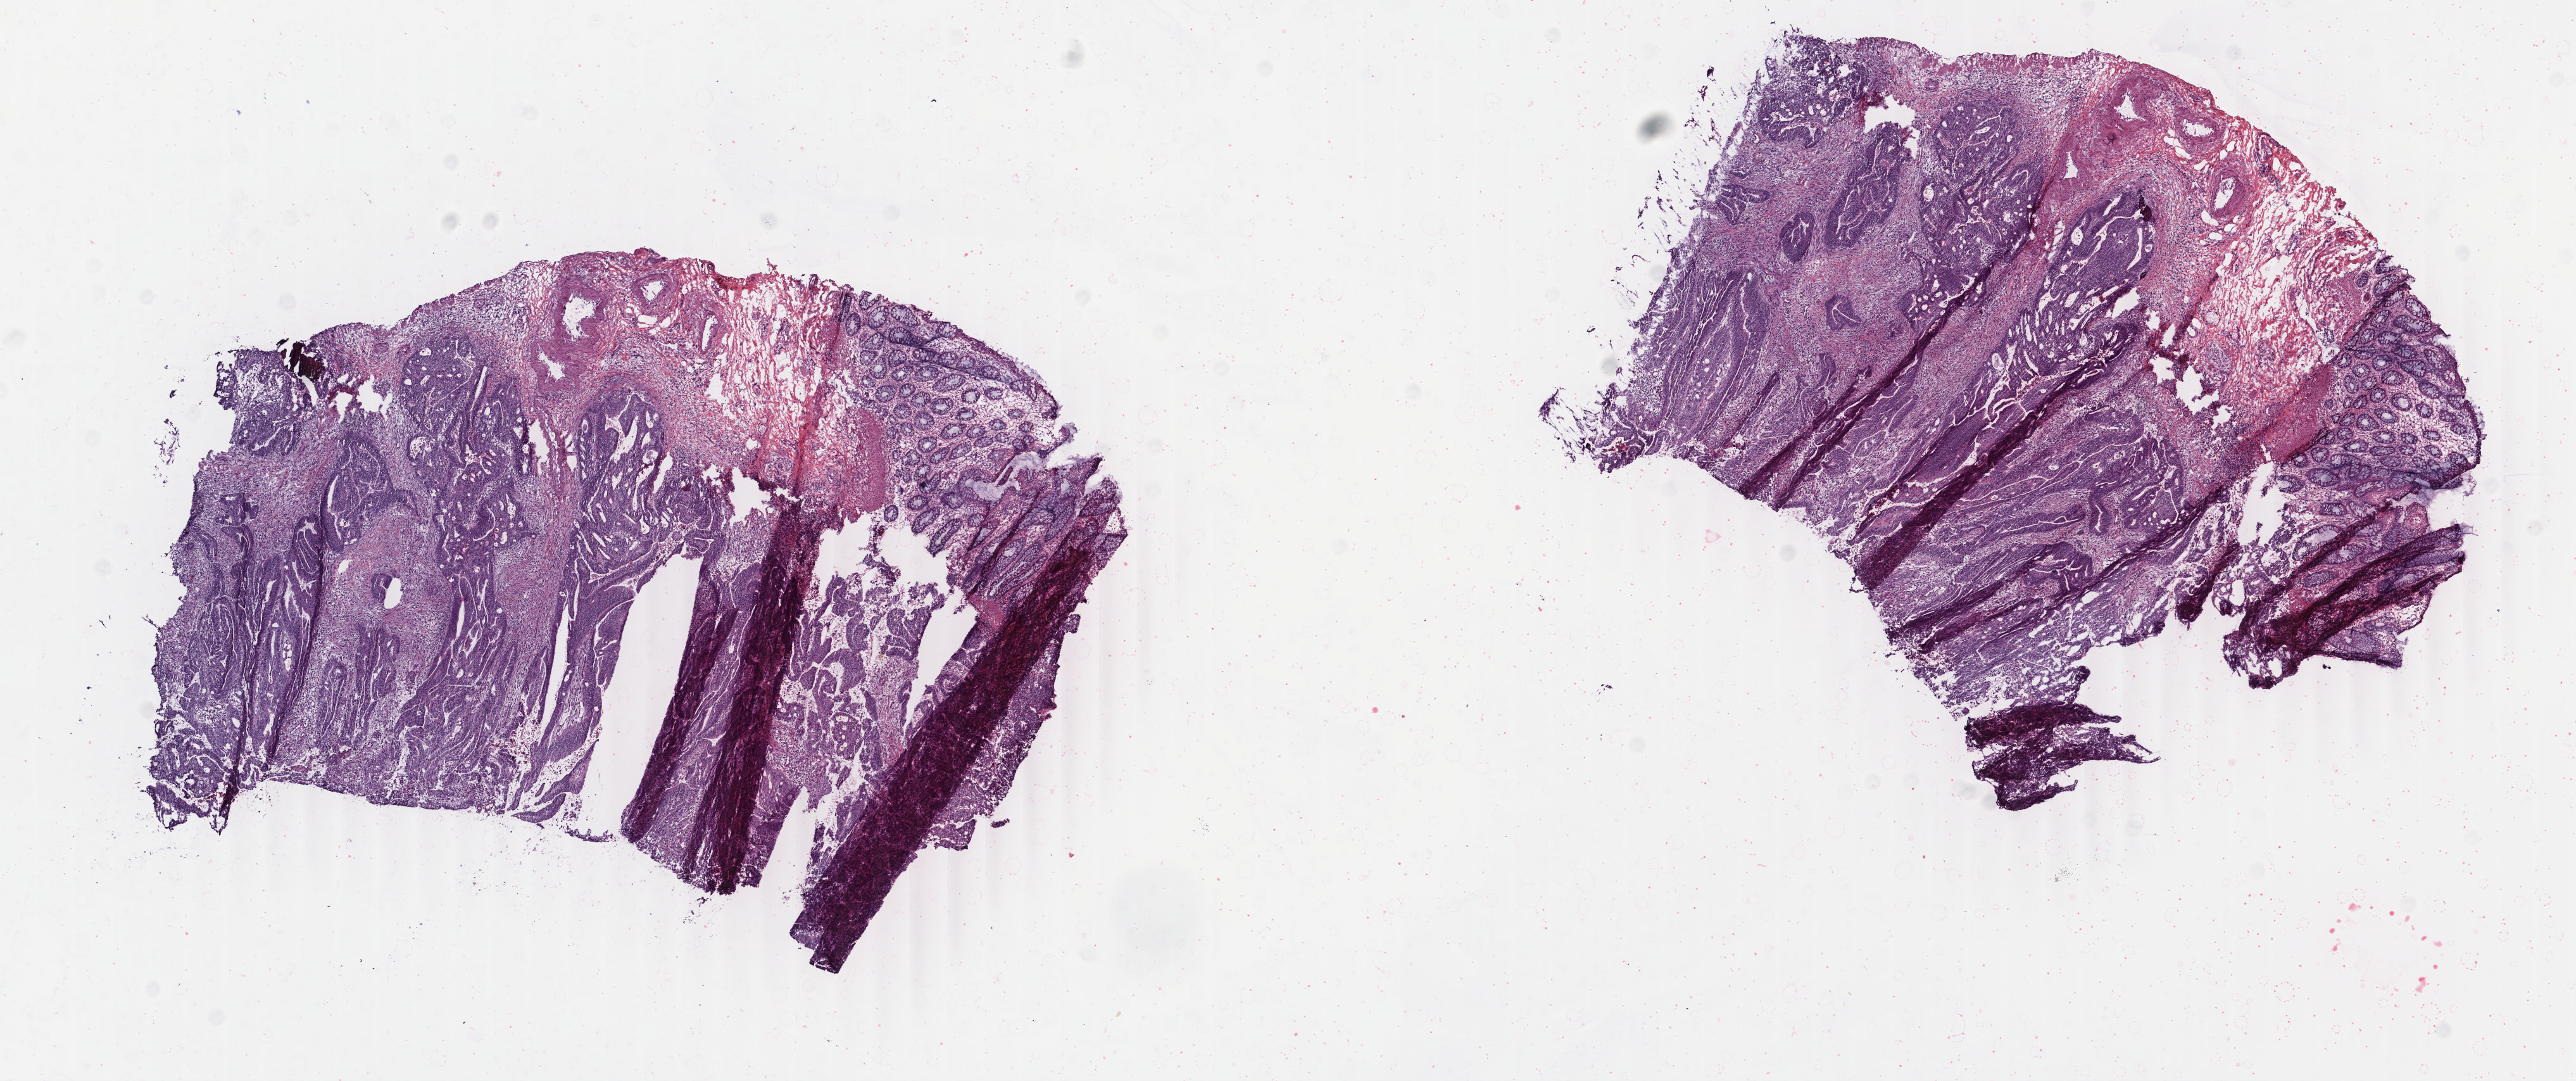
Whole-slide histology image, H&E, low-resolution overview of the scanned area, about 16.2 x 6.8 mm (slide scanned at 40x); frozen section; primary tumour sample from the rectum. Female patient; age at initial diagnosis 59 years. Composition of this section per pathologist review: tumour cells 60%, tumour nuclei 70%.
Diagnosis: Adenocarcinoma, NOS.